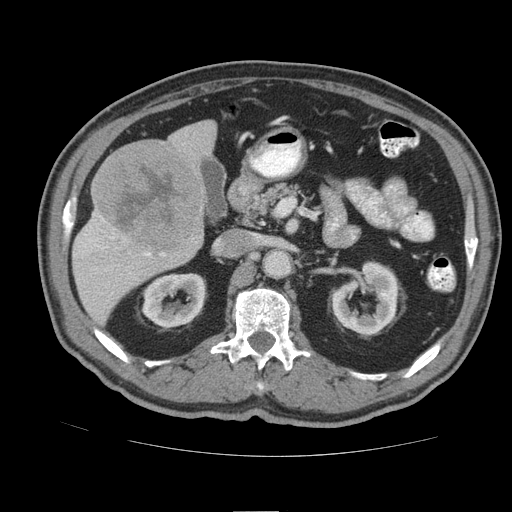
Contrast-enhanced abdominal CT (liver protocol), one axial slice; position 42 of 105 along the scan axis; reconstruction kernel STANDARD; 140 kVp; soft-tissue window (W 400 / L 40 HU); 512 × 512 image matrix. Case-level facts recorded for this patient, not image findings: diagnosis: hepatocellular carcinoma (patient treated with transarterial chemoembolisation; whether this scan precedes or follows treatment is not stated here); TNM stage (as recorded): Stage-IIIB; Child-Pugh class: A; tumour nodularity: multinodular.
Annotated regions visible in this slice (semi-automatically segmented with operator editing):
- liver parenchyma outside the tumour (the mass and vessels are separate outlines, so this box may not span the whole liver): bounding box (x1, y1, x2, y2) in pixels: (72, 120, 216, 324)
- mass: (94, 141, 204, 251)
- liver vessels: (83, 217, 164, 256)